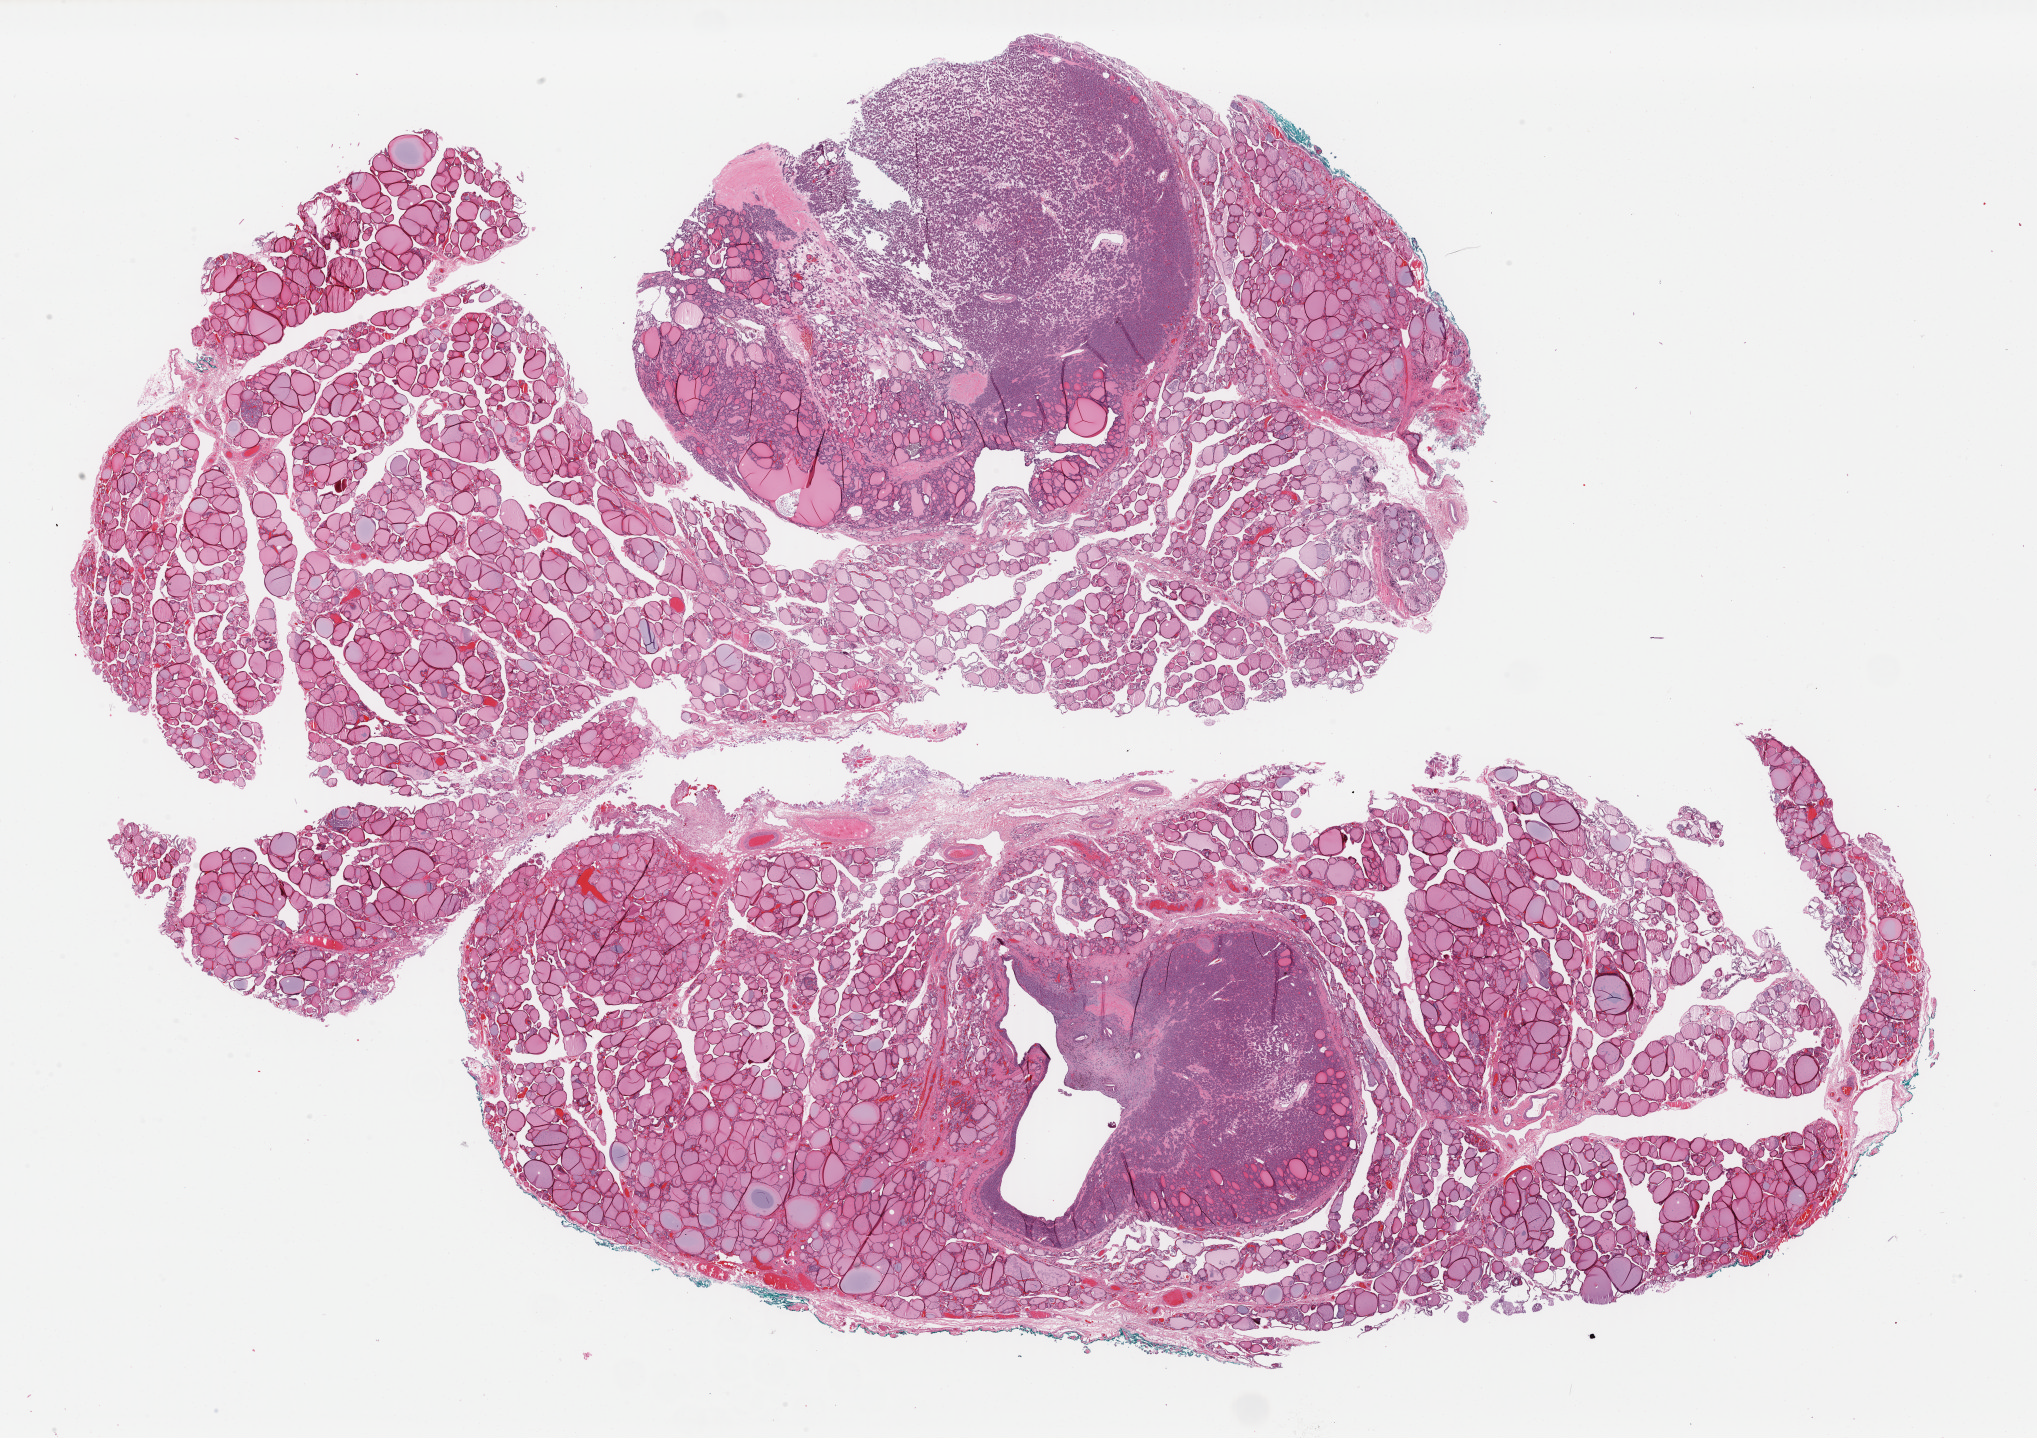
Digitized Hematoxylin and eosin (H&E) stained tissue section (whole slide), shown as a low-resolution overview of the whole scanned area (about 32.1 x 22.7 mm, from a 40x scan), formalin-fixed paraffin-embedded (FFPE) diagnostic section, sample: primary tumour, thyroid. Patient: female, age at initial diagnosis 43 years.
Histologic diagnosis: Papillary carcinoma, follicular variant (thyroid gland). AJCC pathologic stage: I (7th edition).